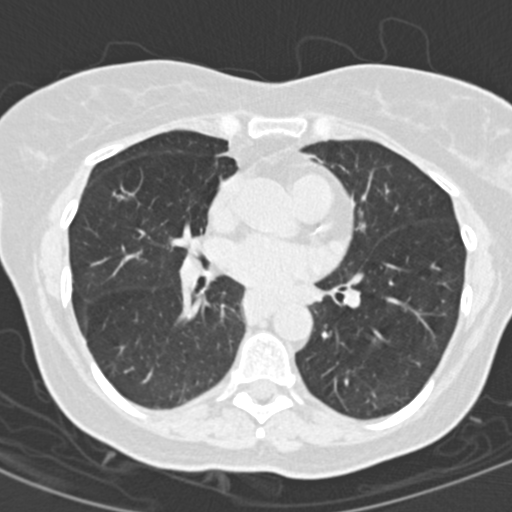
Low-dose screening chest CT, one axial slice; slice 73 of 154 in the series (ordered by position); reconstruction kernel B30f; 120 kVp; lung window (W 1500 / L -600 HU); 2 mm slice thickness; 512 × 512 image matrix, field of view 280 × 280 mm.
Outlined on this slice (outlined manually by an expert reader):
- lesion 2 (nodule, middle lobe of right lung): bounding box <112,187,126,199> (left, top, right, bottom; pixels)